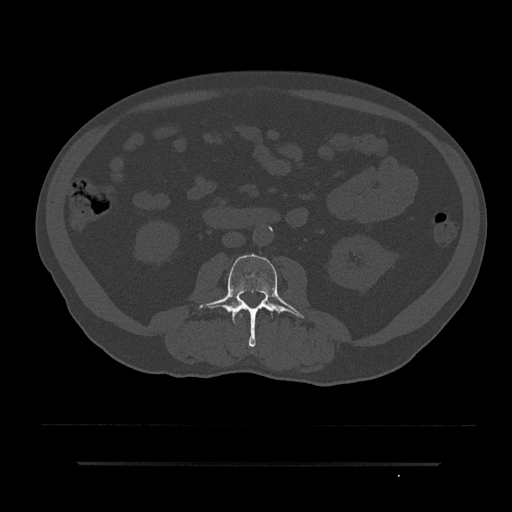
CT including the spine, one axial slice; slice 10 of 797 in the series (ordered by position); reconstruction kernel Br40s/3; 120 kVp; bone window (W 1800 / L 400 HU); 0.5 mm slice thickness; 512 × 512 image matrix. Male patient, age 59 years. From the clinical record (not read from this slice): primary cancer: bile ducts.
Structures marked on this image (semi-automatically segmented with operator editing):
- L2 vertebra: bounding box (x1, y1, x2, y2) in pixels: (239, 308, 250, 318)
- L3 vertebra: (198, 254, 305, 347)